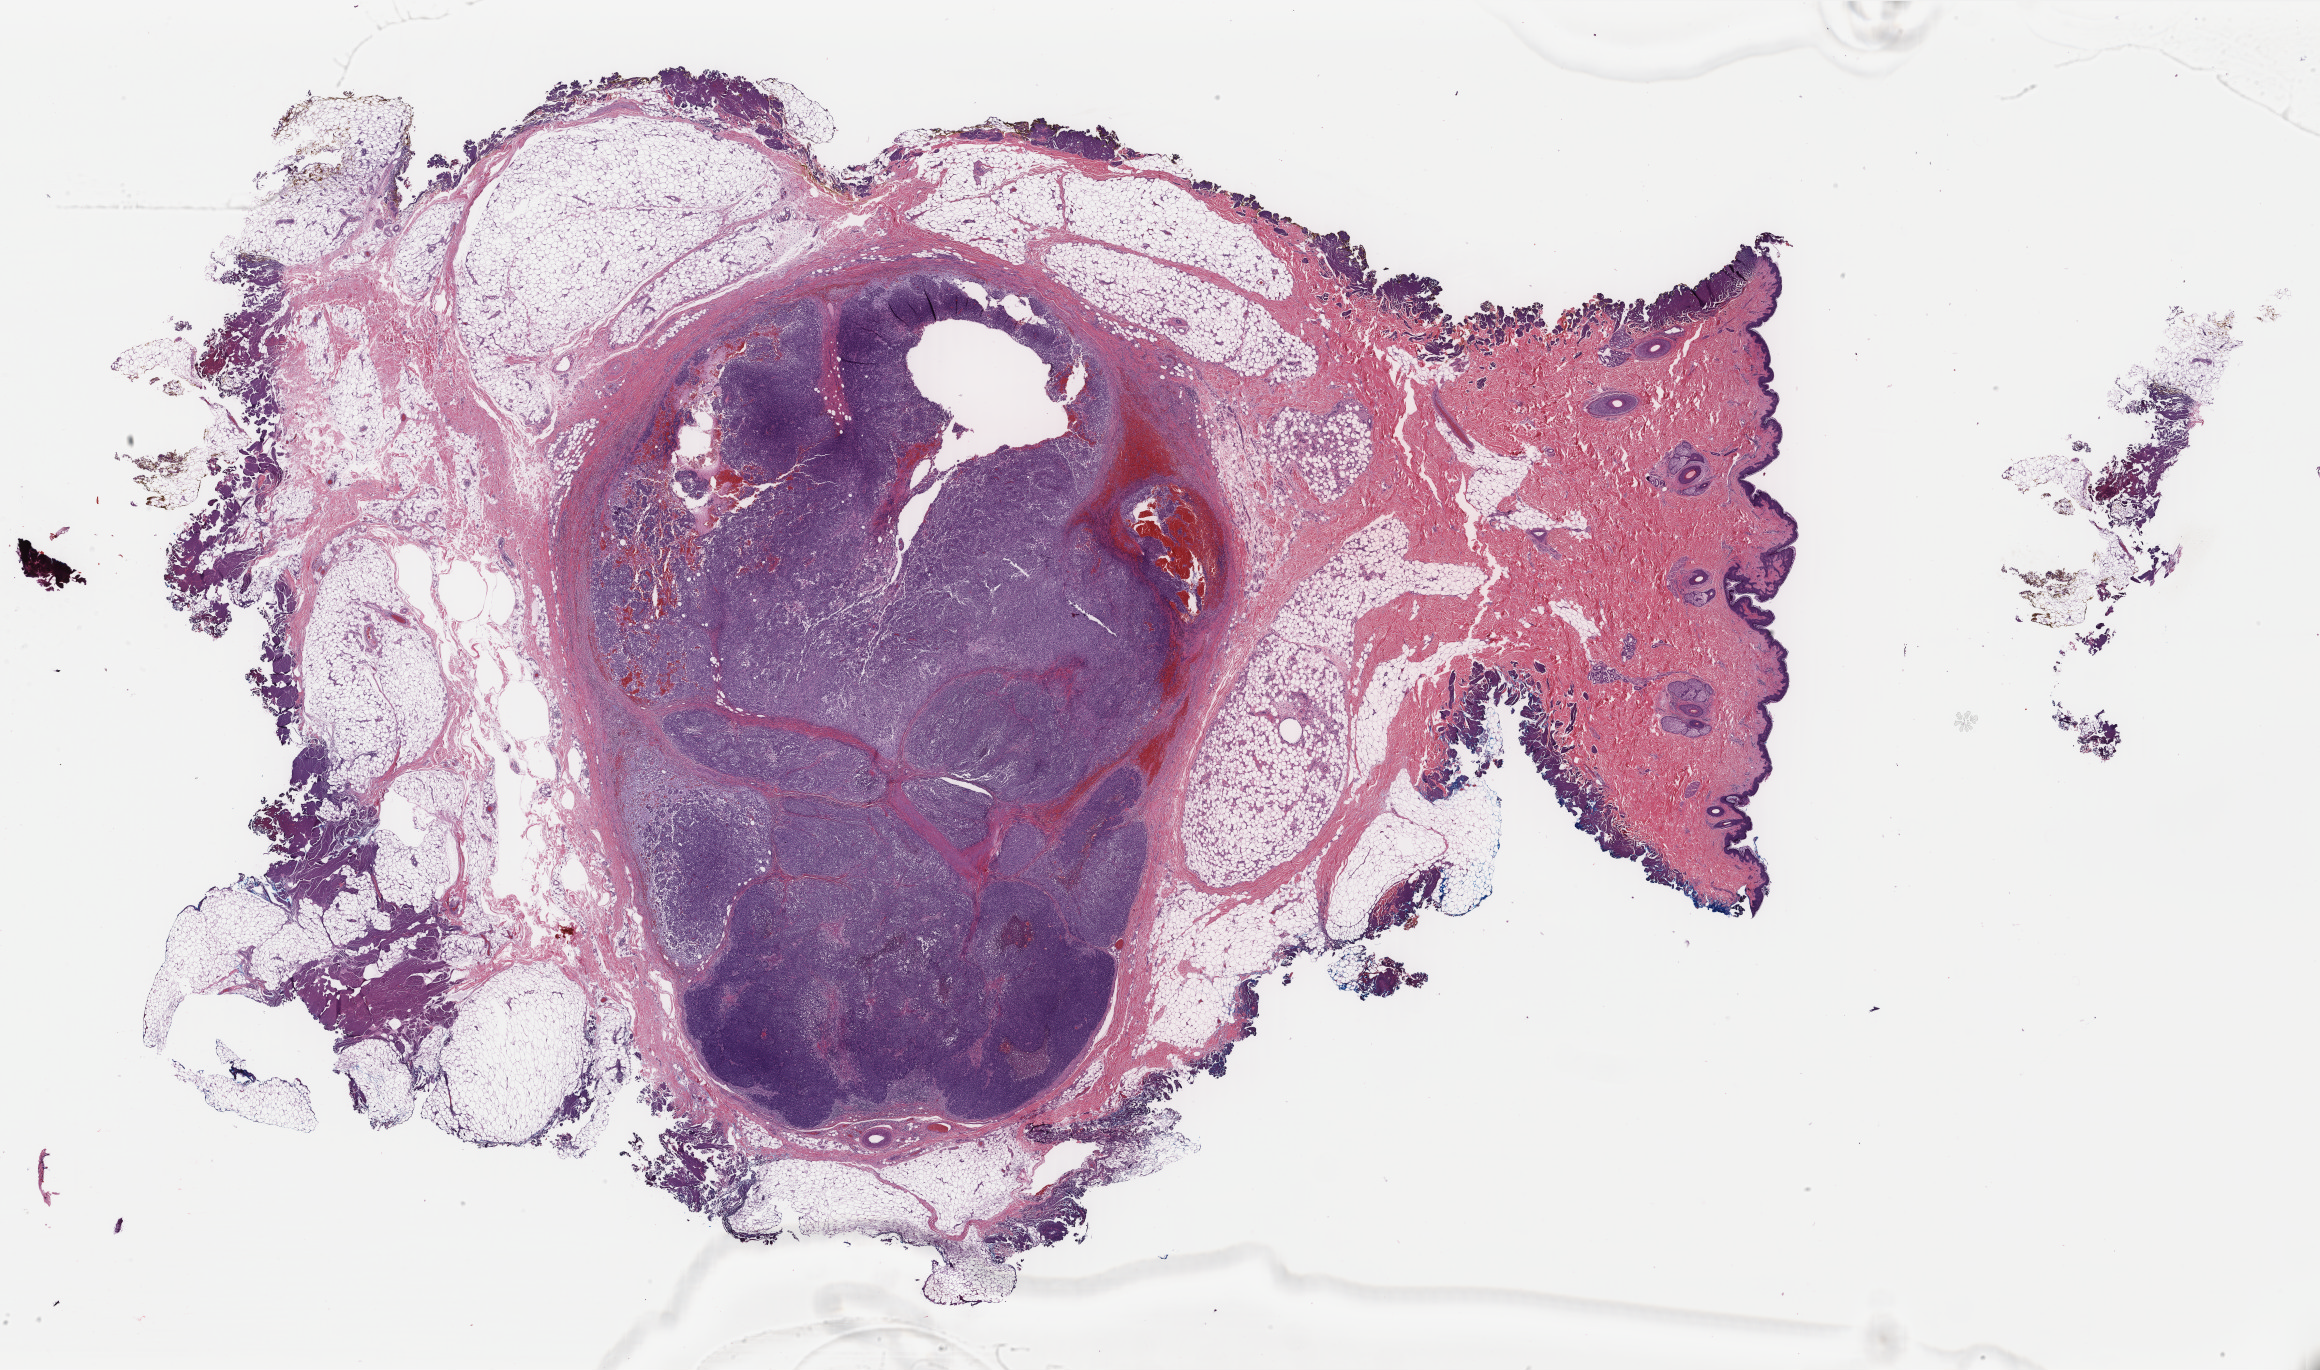
Digitized H&E tissue section (whole slide) — a low-resolution overview of the entire scanned area, about 36.8 x 21.7 mm (slide scanned at 40x); formalin-fixed paraffin-embedded (FFPE) diagnostic section; sample: primary tumour, skin. Male patient; age at initial diagnosis 46 years.
Diagnosis: Malignant melanoma, NOS.